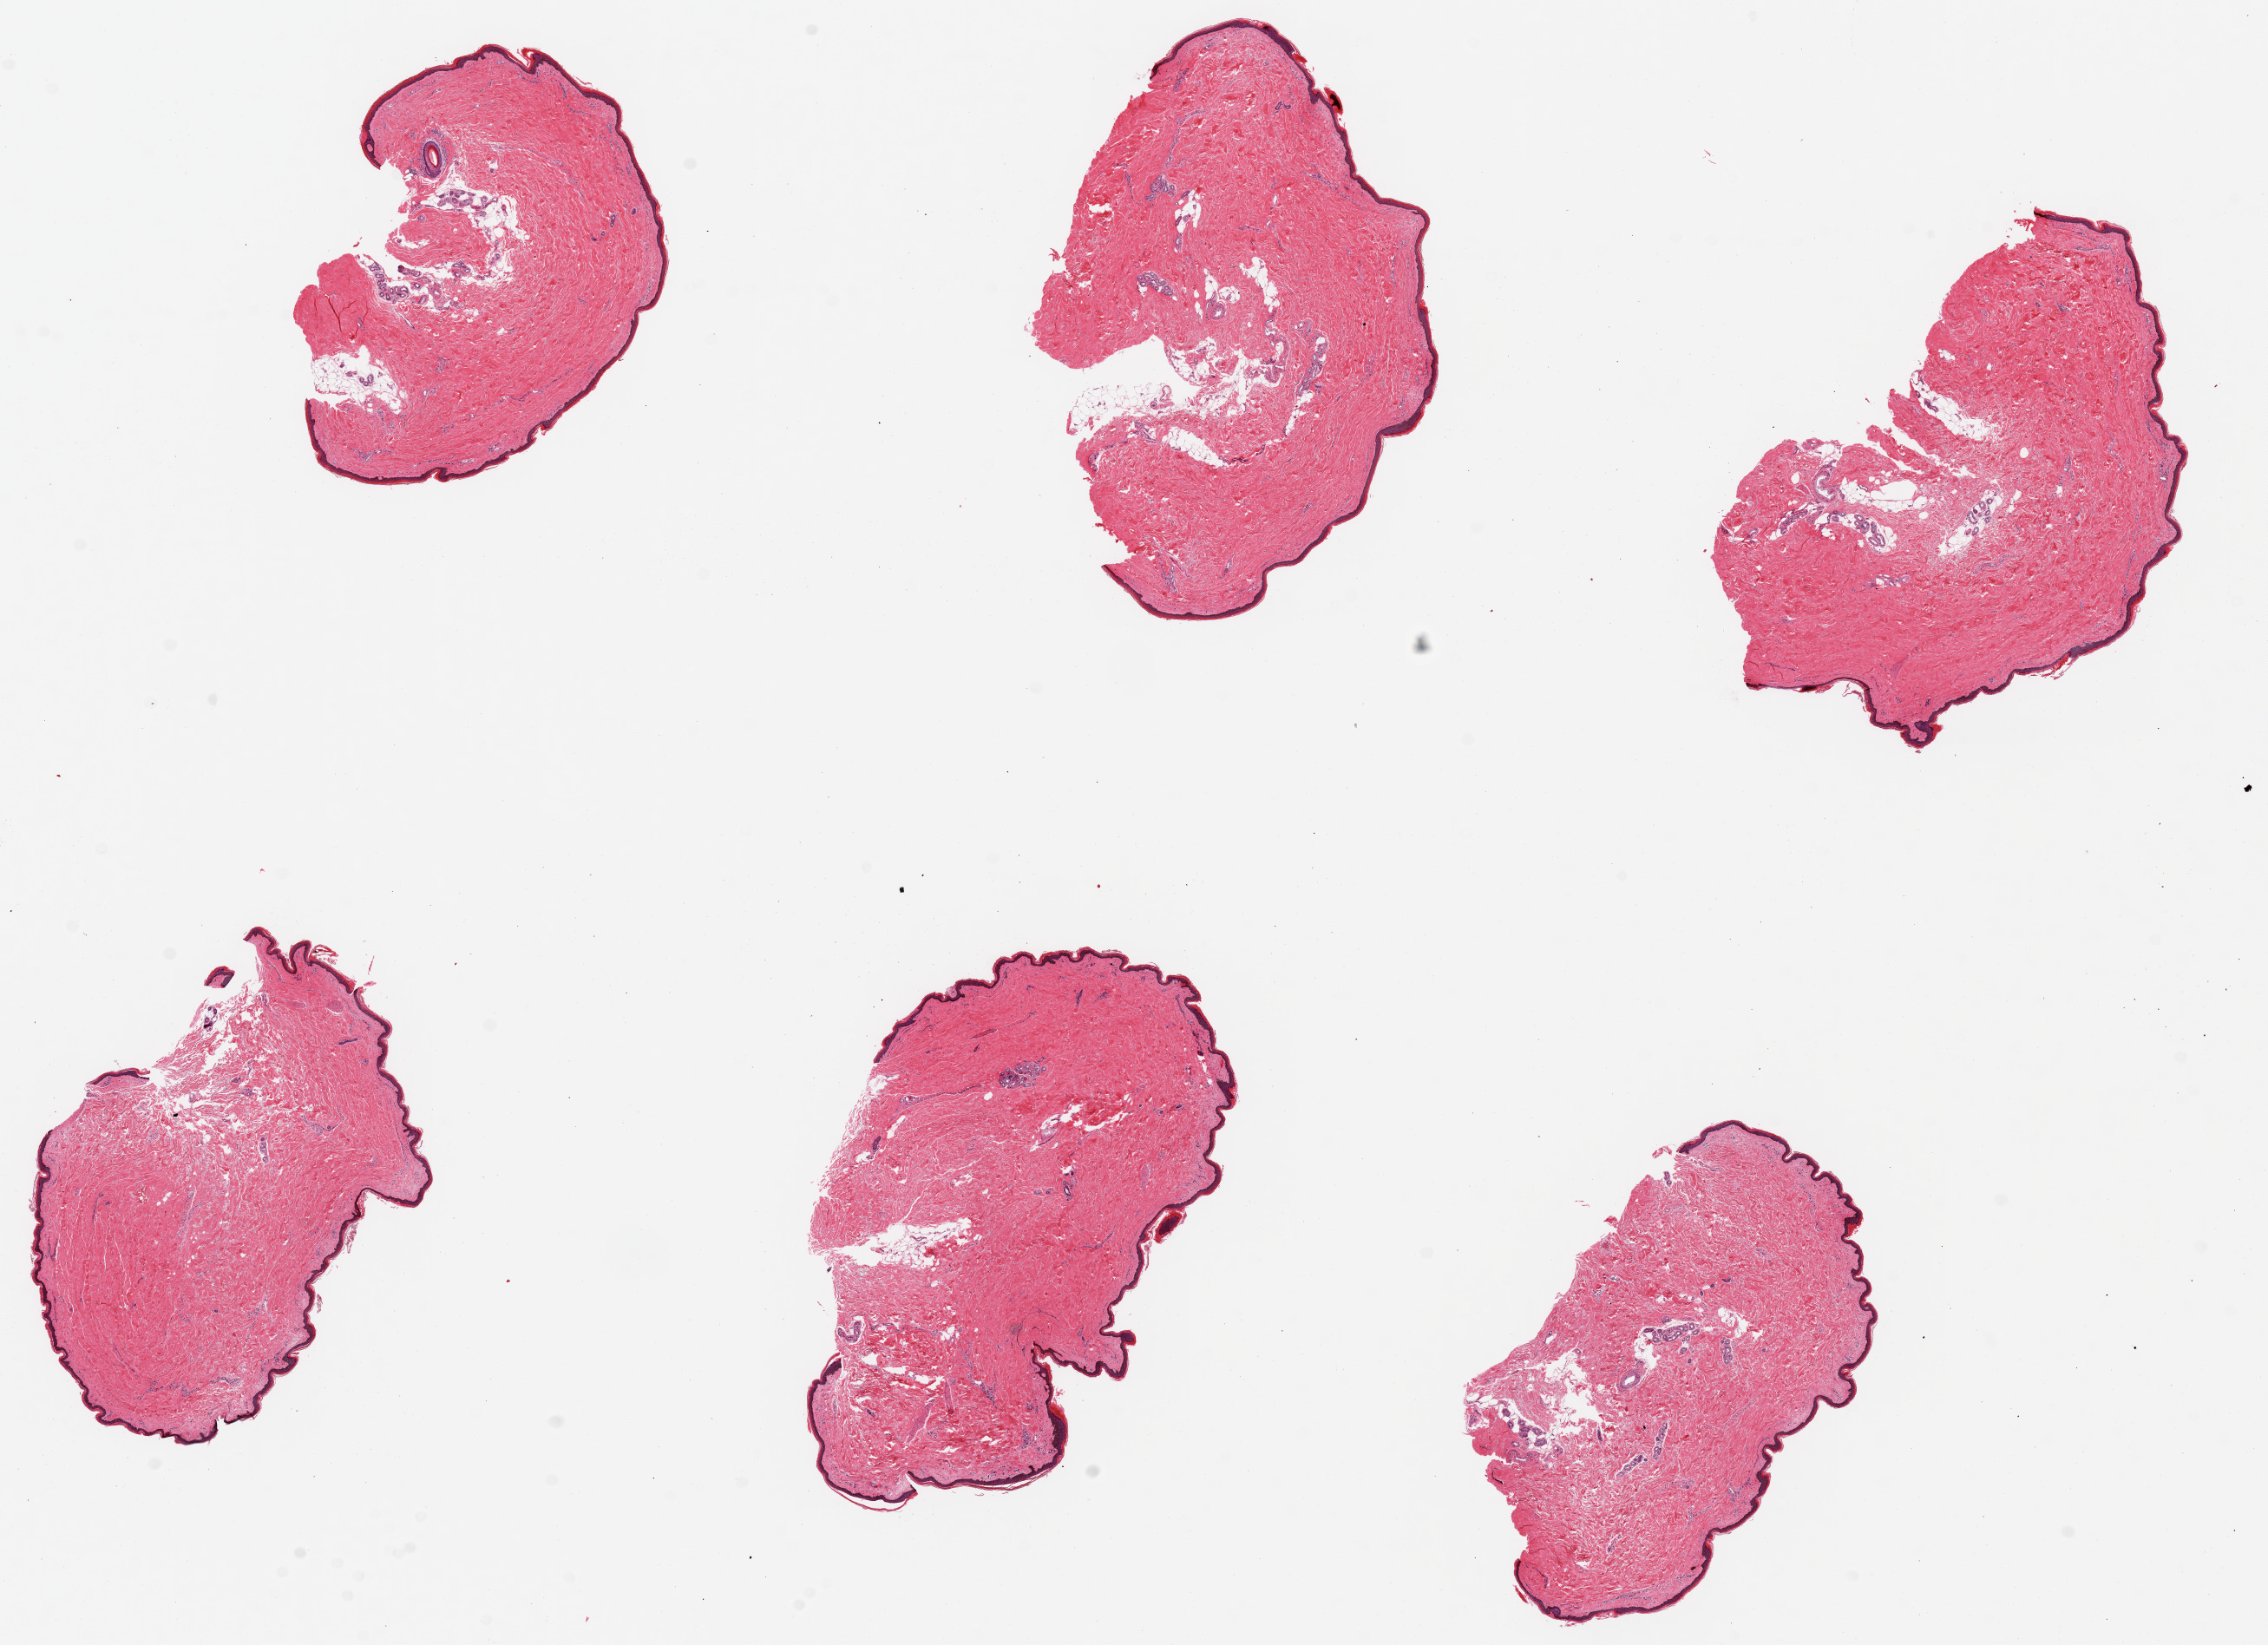
Digitized haematoxylin and eosin-stained section — whole scanned area (about 20.7 x 15.0 mm, from a 20x scan) shown as a low-resolution overview, PAXgene-fixed paraffin-embedded (PFPE) section, target tissue: skin of lower leg, donor tissue sample. Donor: female.
Review note (as recorded): 6 pieces, up to 5.5x3mm; Squamous epithelium ~2% thicknesss.